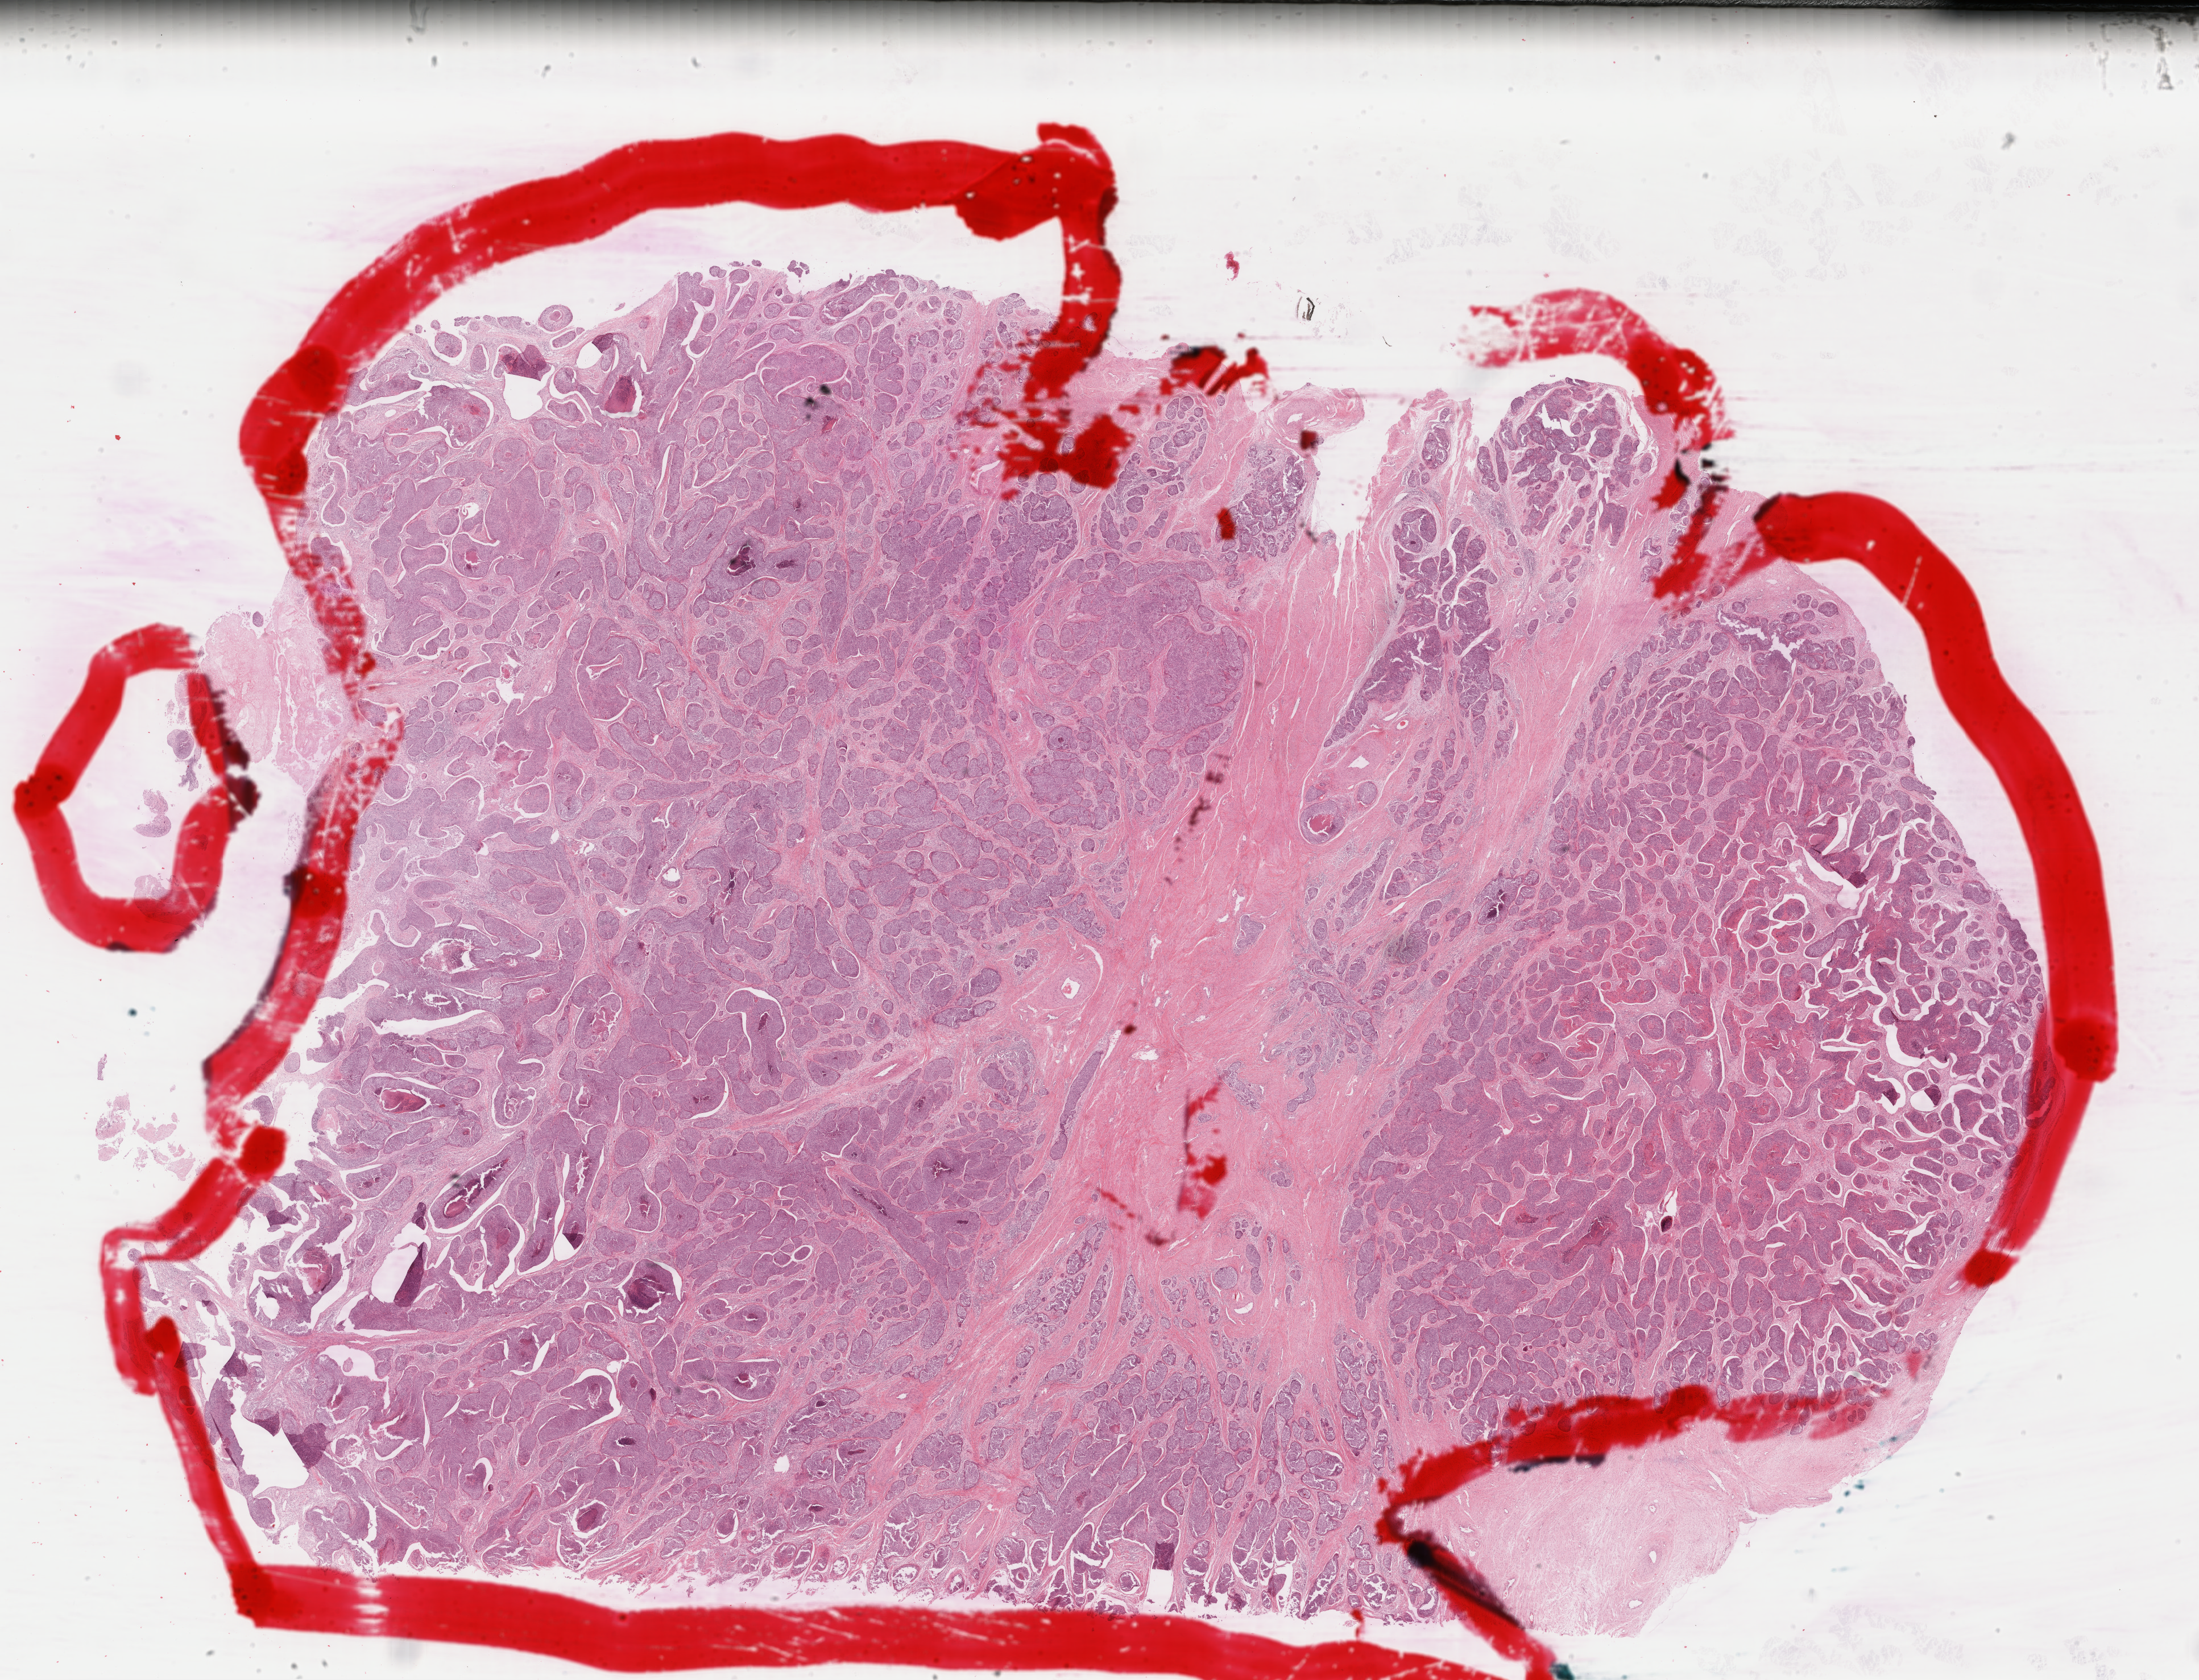
Digitized H&E tissue section (whole slide) — a low-resolution overview of the entire scanned area, about 30.7 x 23.4 mm. Formalin-fixed paraffin-embedded (FFPE) diagnostic section. Primary tumour sample from the cervix. Female patient; age at initial diagnosis 35 years. Histologic grade: G1 (well differentiated).
Pathologic diagnosis: Squamous cell carcinoma, NOS. FIGO stage: IB.